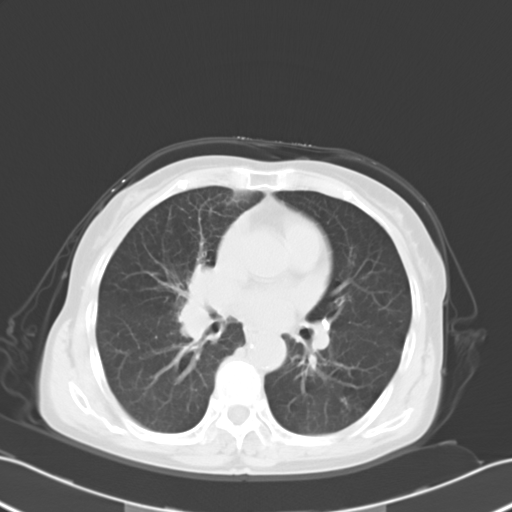
Chest CT, one axial slice; position 14 of 27 along the scan axis; reconstruction kernel B40f; 120 kVp; lung window (W 1500 / L -600 HU); 10 mm slice thickness; 512 × 512 image matrix, field of view 353 × 353 mm. Female patient, age 67 years. Case-level facts recorded for this patient, not image findings: clinical TNM (as recorded): T2a N3 M0.
Annotated regions visible in this slice (rectangle marked by the reading radiologist):
- lung tumour (recorded histology: small cell carcinoma): bounding box (x1, y1, x2, y2) in pixels: (169, 259, 217, 341)